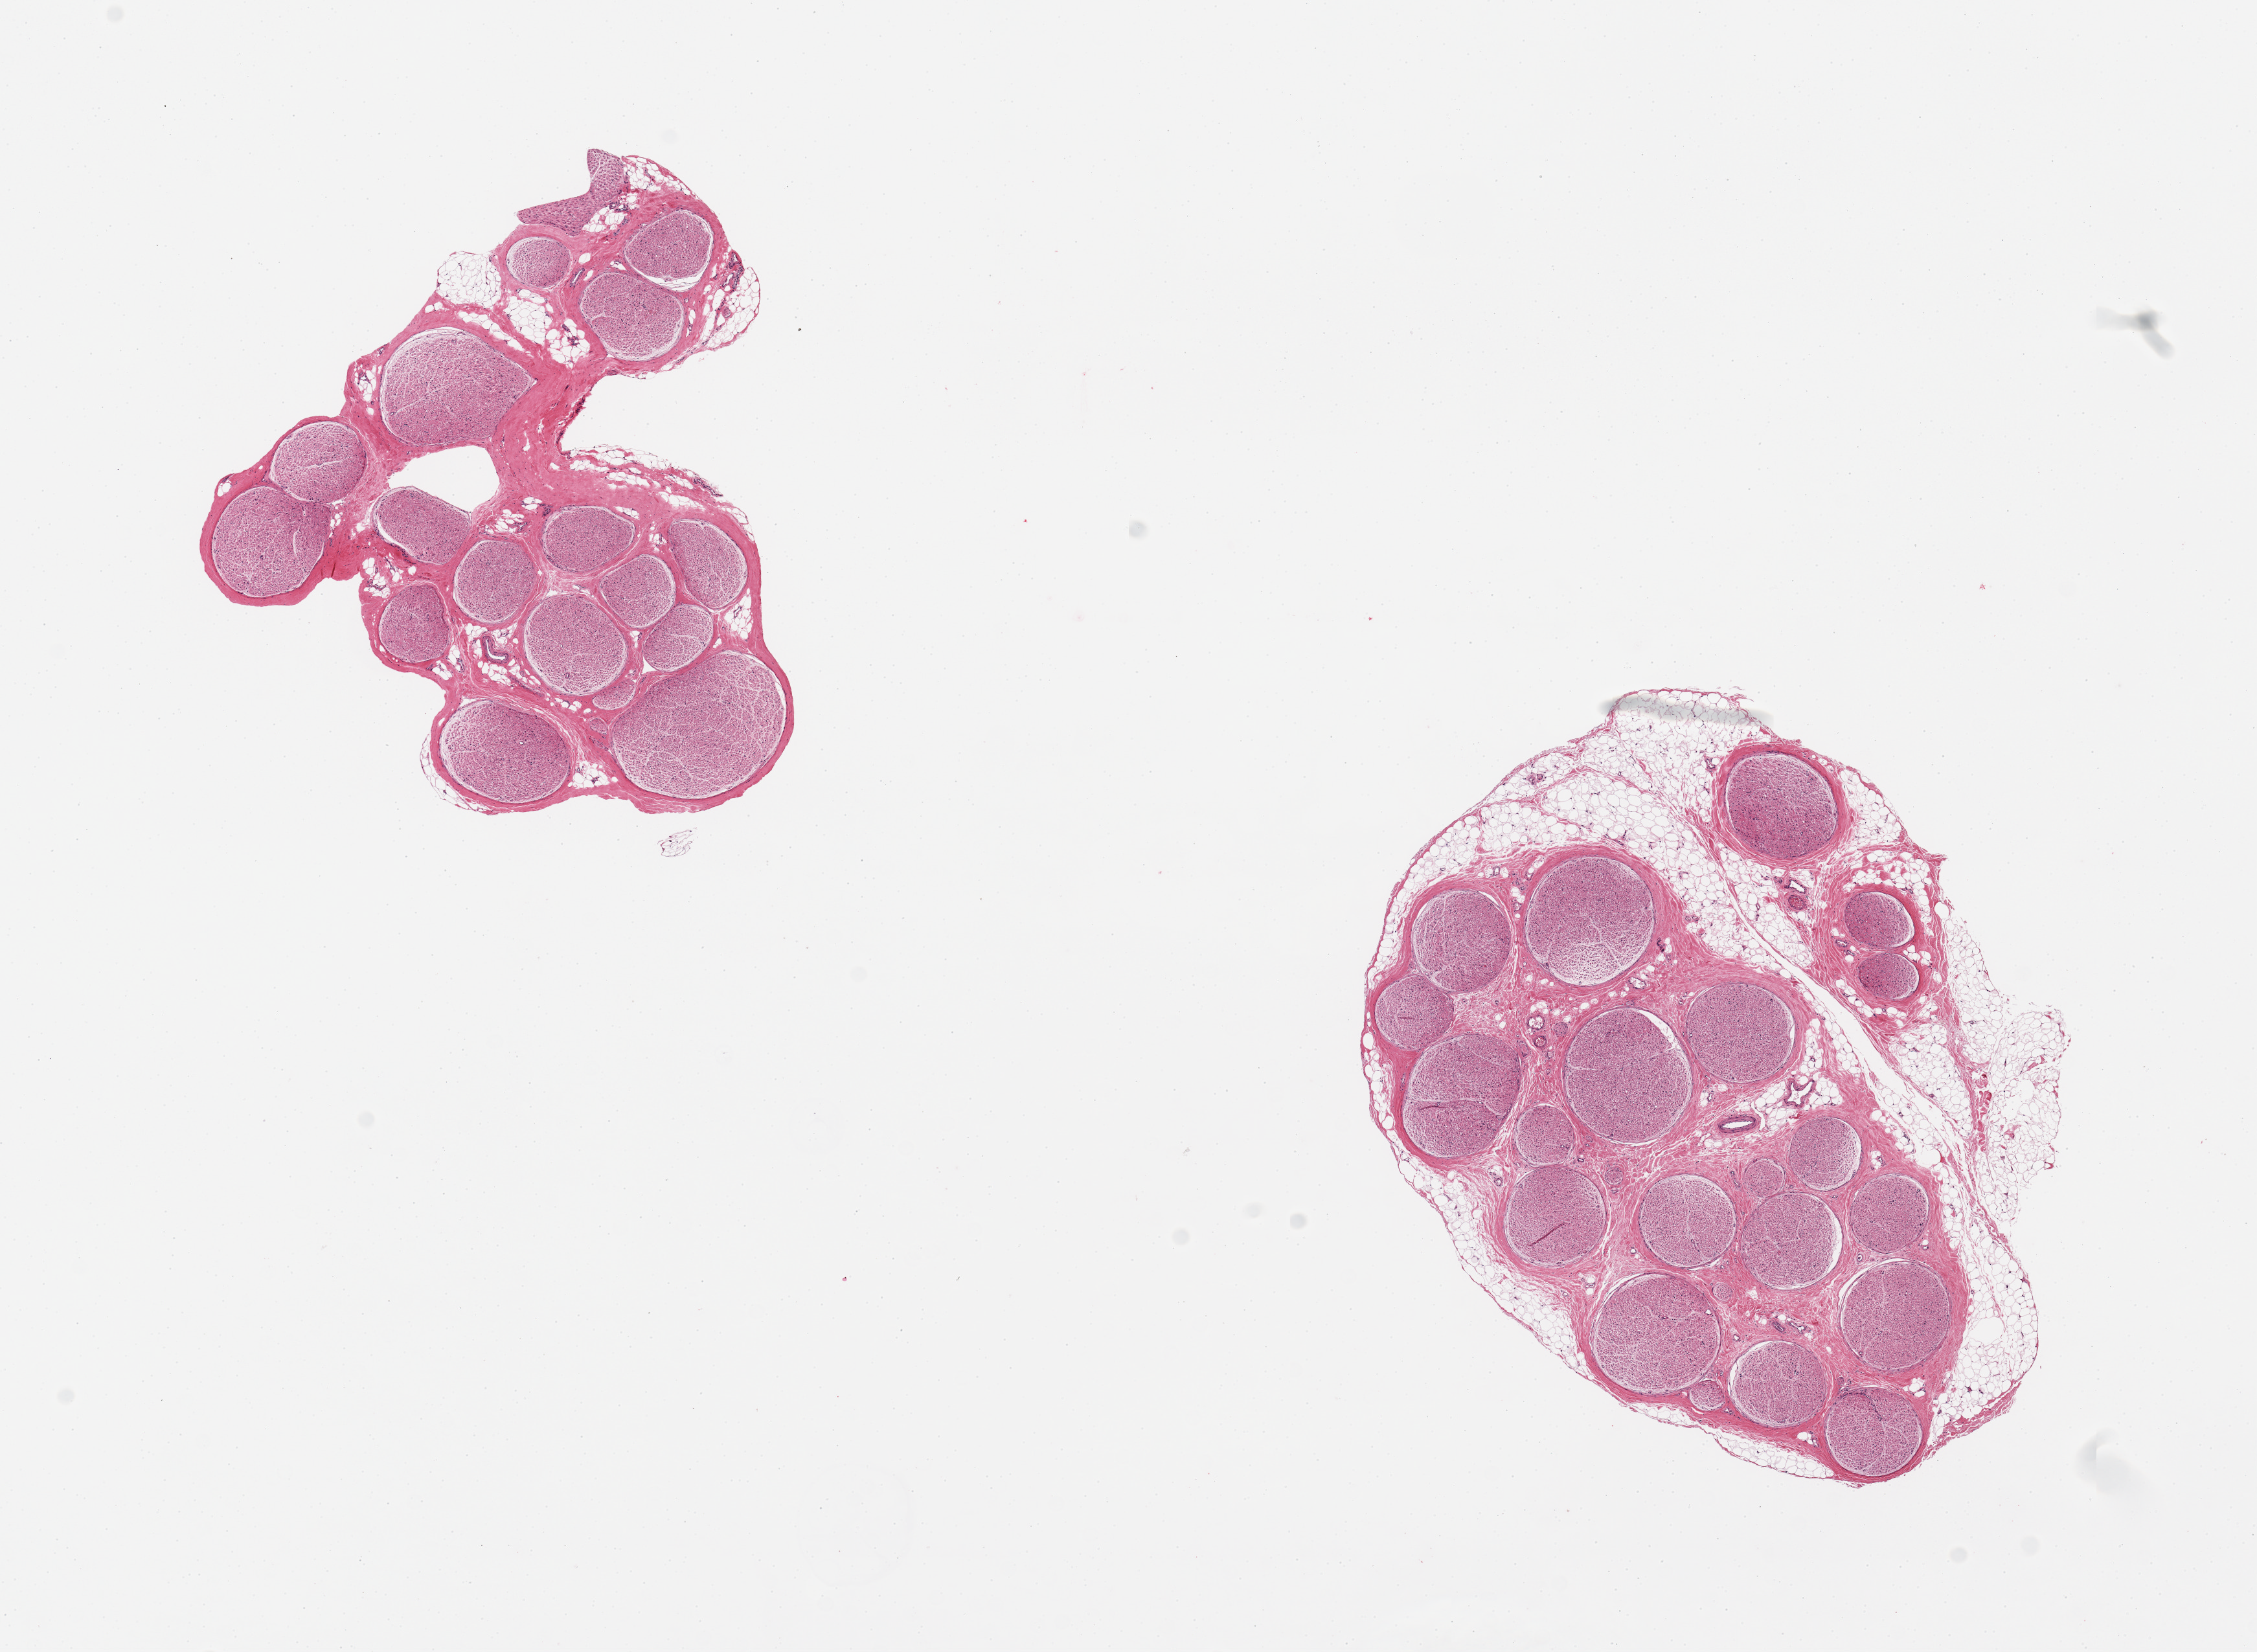
Haematoxylin and eosin whole-slide image — low-resolution overview of the scanned area, about 13.8 x 10.1 mm; PAXgene-fixed paraffin-embedded (PFPE) section; target tissue: tibial nerve; donor tissue sample. Female donor.
- review note (as recorded): 2 pieces, focal adhrent fat ~0.6mm